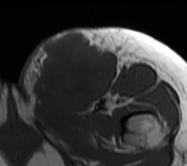
MRI of an extremity soft-tissue mass, one axial slice. Position 24 of 62 along the scan axis. MR volume resampled by the dataset authors to the PET/CT grid (not the native acquisition matrix). 3.27 mm slice thickness. 187 × 166 image matrix, field of view 183 × 162 mm. Female patient. From the clinical record (not read from this slice): histological type: leiomyosarcoma; grade: high; site of the primary tumour: groin.
Outlined on this slice (expert contour drawn on MRI and transferred to this co-registered scan by the dataset authors):
- gross tumour volume including surrounding oedema: bounding box (x1, y1, x2, y2) in pixels: (18, 28, 131, 107)
- gross tumour volume (mass): (36, 33, 115, 107)